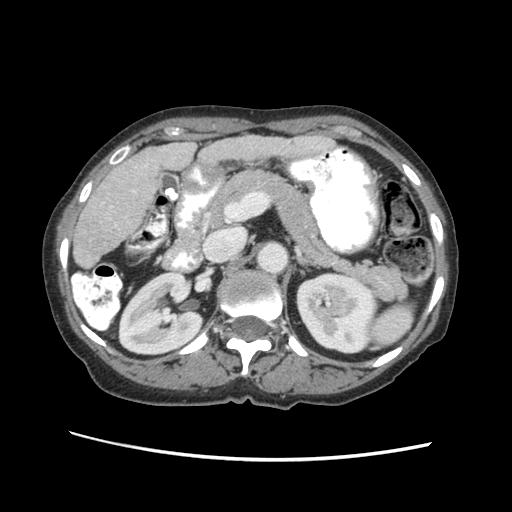
Contrast-enhanced abdominal CT (liver protocol), one axial slice. Slice 22 of 63 in the series (ordered by position). Reconstruction kernel STANDARD. Soft-tissue window (W 400 / L 40 HU). 2.5 mm slice thickness. 512 × 512 image matrix, field of view 340 × 340 mm. From the clinical record (not read from this slice): diagnosis: hepatocellular carcinoma (patient treated with transarterial chemoembolisation; whether this scan precedes or follows treatment is not stated here); TNM stage (as recorded): Stage-I; Child-Pugh class: B; tumour nodularity: uninodular.
Annotated regions visible in this slice (semi-automatic segmentation, software-assisted and operator-edited):
- liver parenchyma outside the tumour (the mass and vessels are separate outlines, so this box may not span the whole liver): box from (x=72, y=130) to (x=332, y=266) px